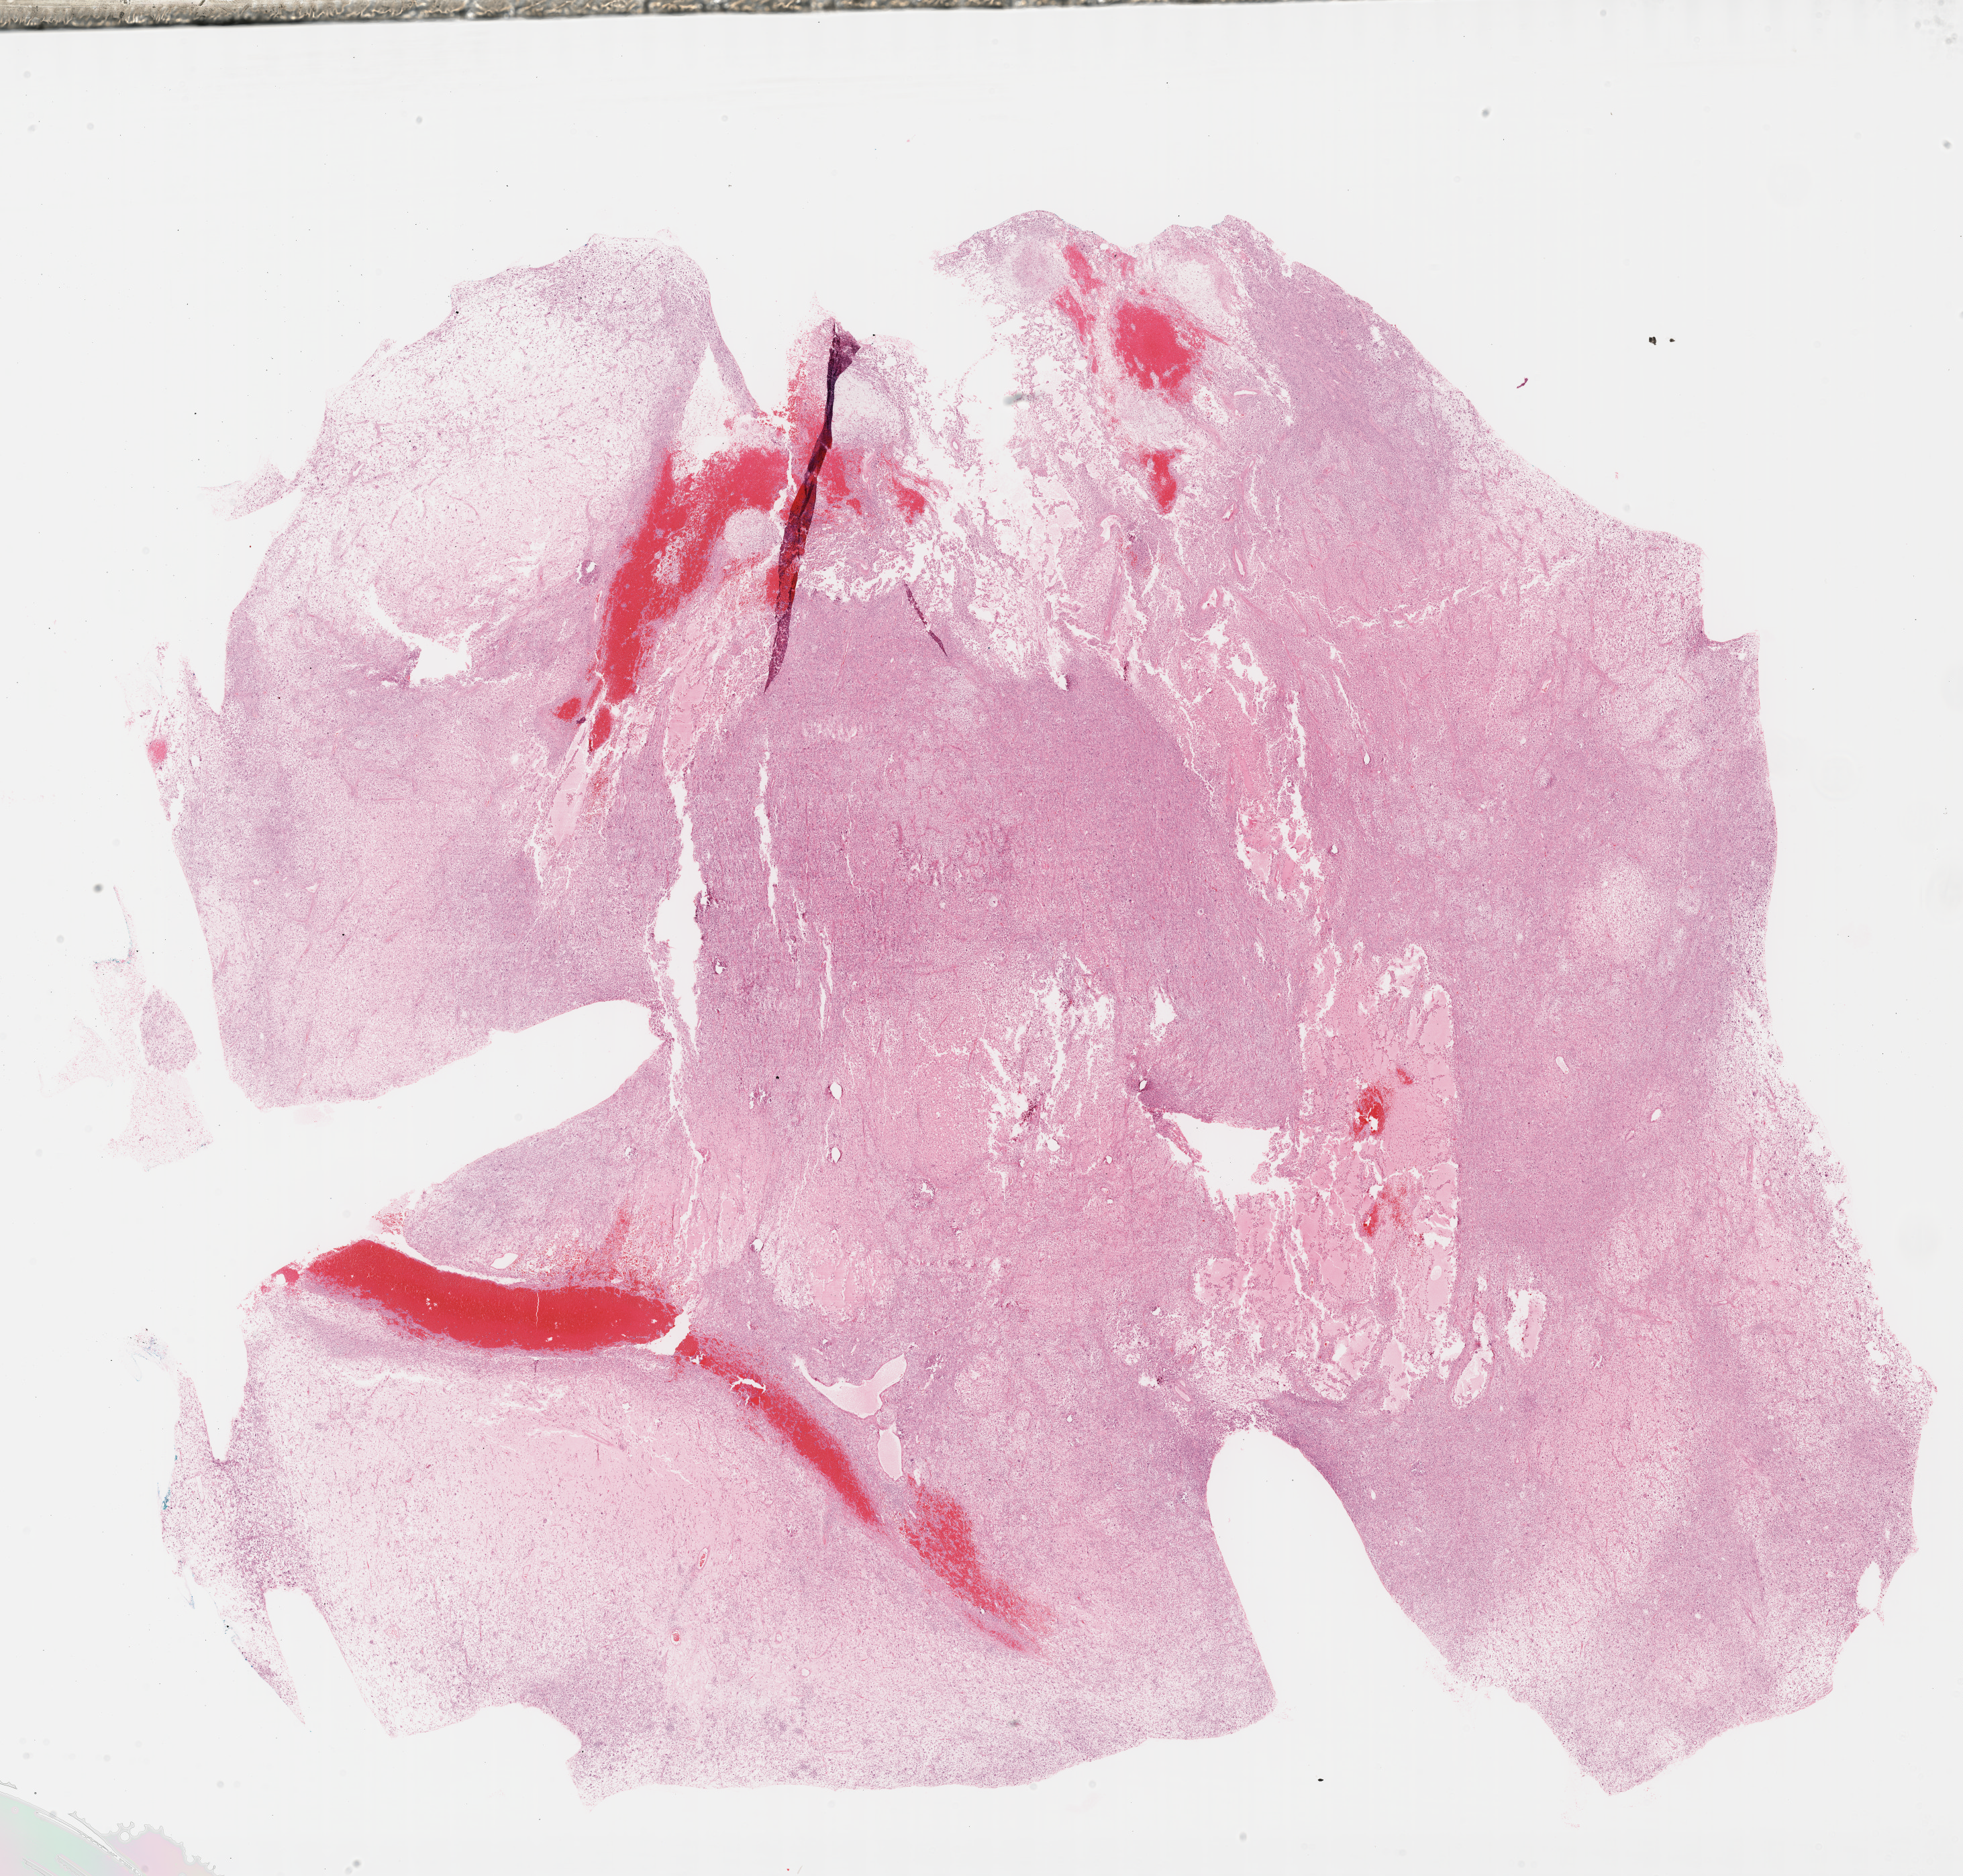
Digitized H&E tissue section (whole slide) — low-resolution overview of the scanned area, about 23.6 x 22.6 mm (acquisition: 40x scan), formalin-fixed paraffin-embedded (FFPE) diagnostic section, connective, subcutaneous and other soft tissues, primary tumour sample. Female patient; age at initial diagnosis 63 years.
Pathologic diagnosis: Malignant fibrous histiocytoma (connective, subcutaneous and other soft tissues of lower limb and hip).